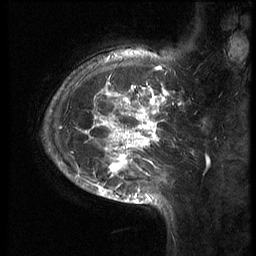
Breast MRI (dynamic contrast-enhanced), one sagittal slice. Position 17 of 70 along the scan axis. 3 images stored at this slice position (order not interpretable as contrast timing). 1.5 T. TE 4.2 ms, TR 9 ms. 256 × 256 image matrix, field of view 180 × 180 mm. Female patient, age 28 years. From the clinical record (not read from this slice): setting: breast cancer imaged before/during neoadjuvant chemotherapy.
Annotated regions visible in this slice (semi-automatically segmented with operator editing):
- analysis volume of interest (the breast-tissue region the enhancement analysis was run in; not a lesion): bounding box (x1, y1, x2, y2) in pixels: (43, 42, 186, 215)
- tumour enhancement mask (voxels above the 140 % enhancement threshold inside the analysis volume of interest): (62, 52, 180, 205)